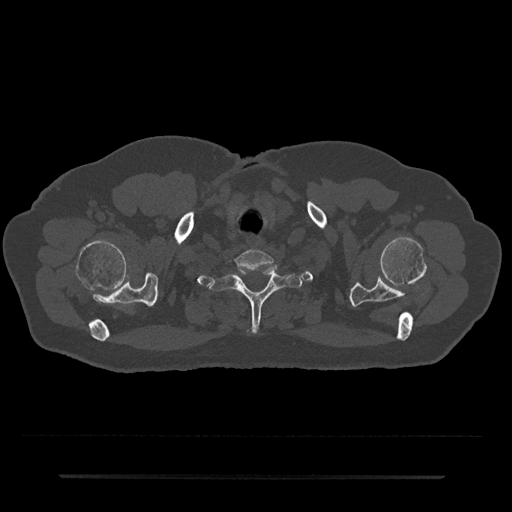
CT including the spine, one axial slice; position 647 of 797 along the scan axis; reconstruction kernel Br40s/3; 120 kVp; bone window (W 1800 / L 400 HU); 0.5 mm slice thickness; 512 × 512 image matrix. Patient: male, 69 years. Case-level facts recorded for this patient, not image findings: primary cancer: prostate.
Annotated regions visible in this slice (semi-automatic segmentation, software-assisted and operator-edited):
- T1 vertebra: bounding box (x1, y1, x2, y2) in pixels: (209, 267, 303, 328)